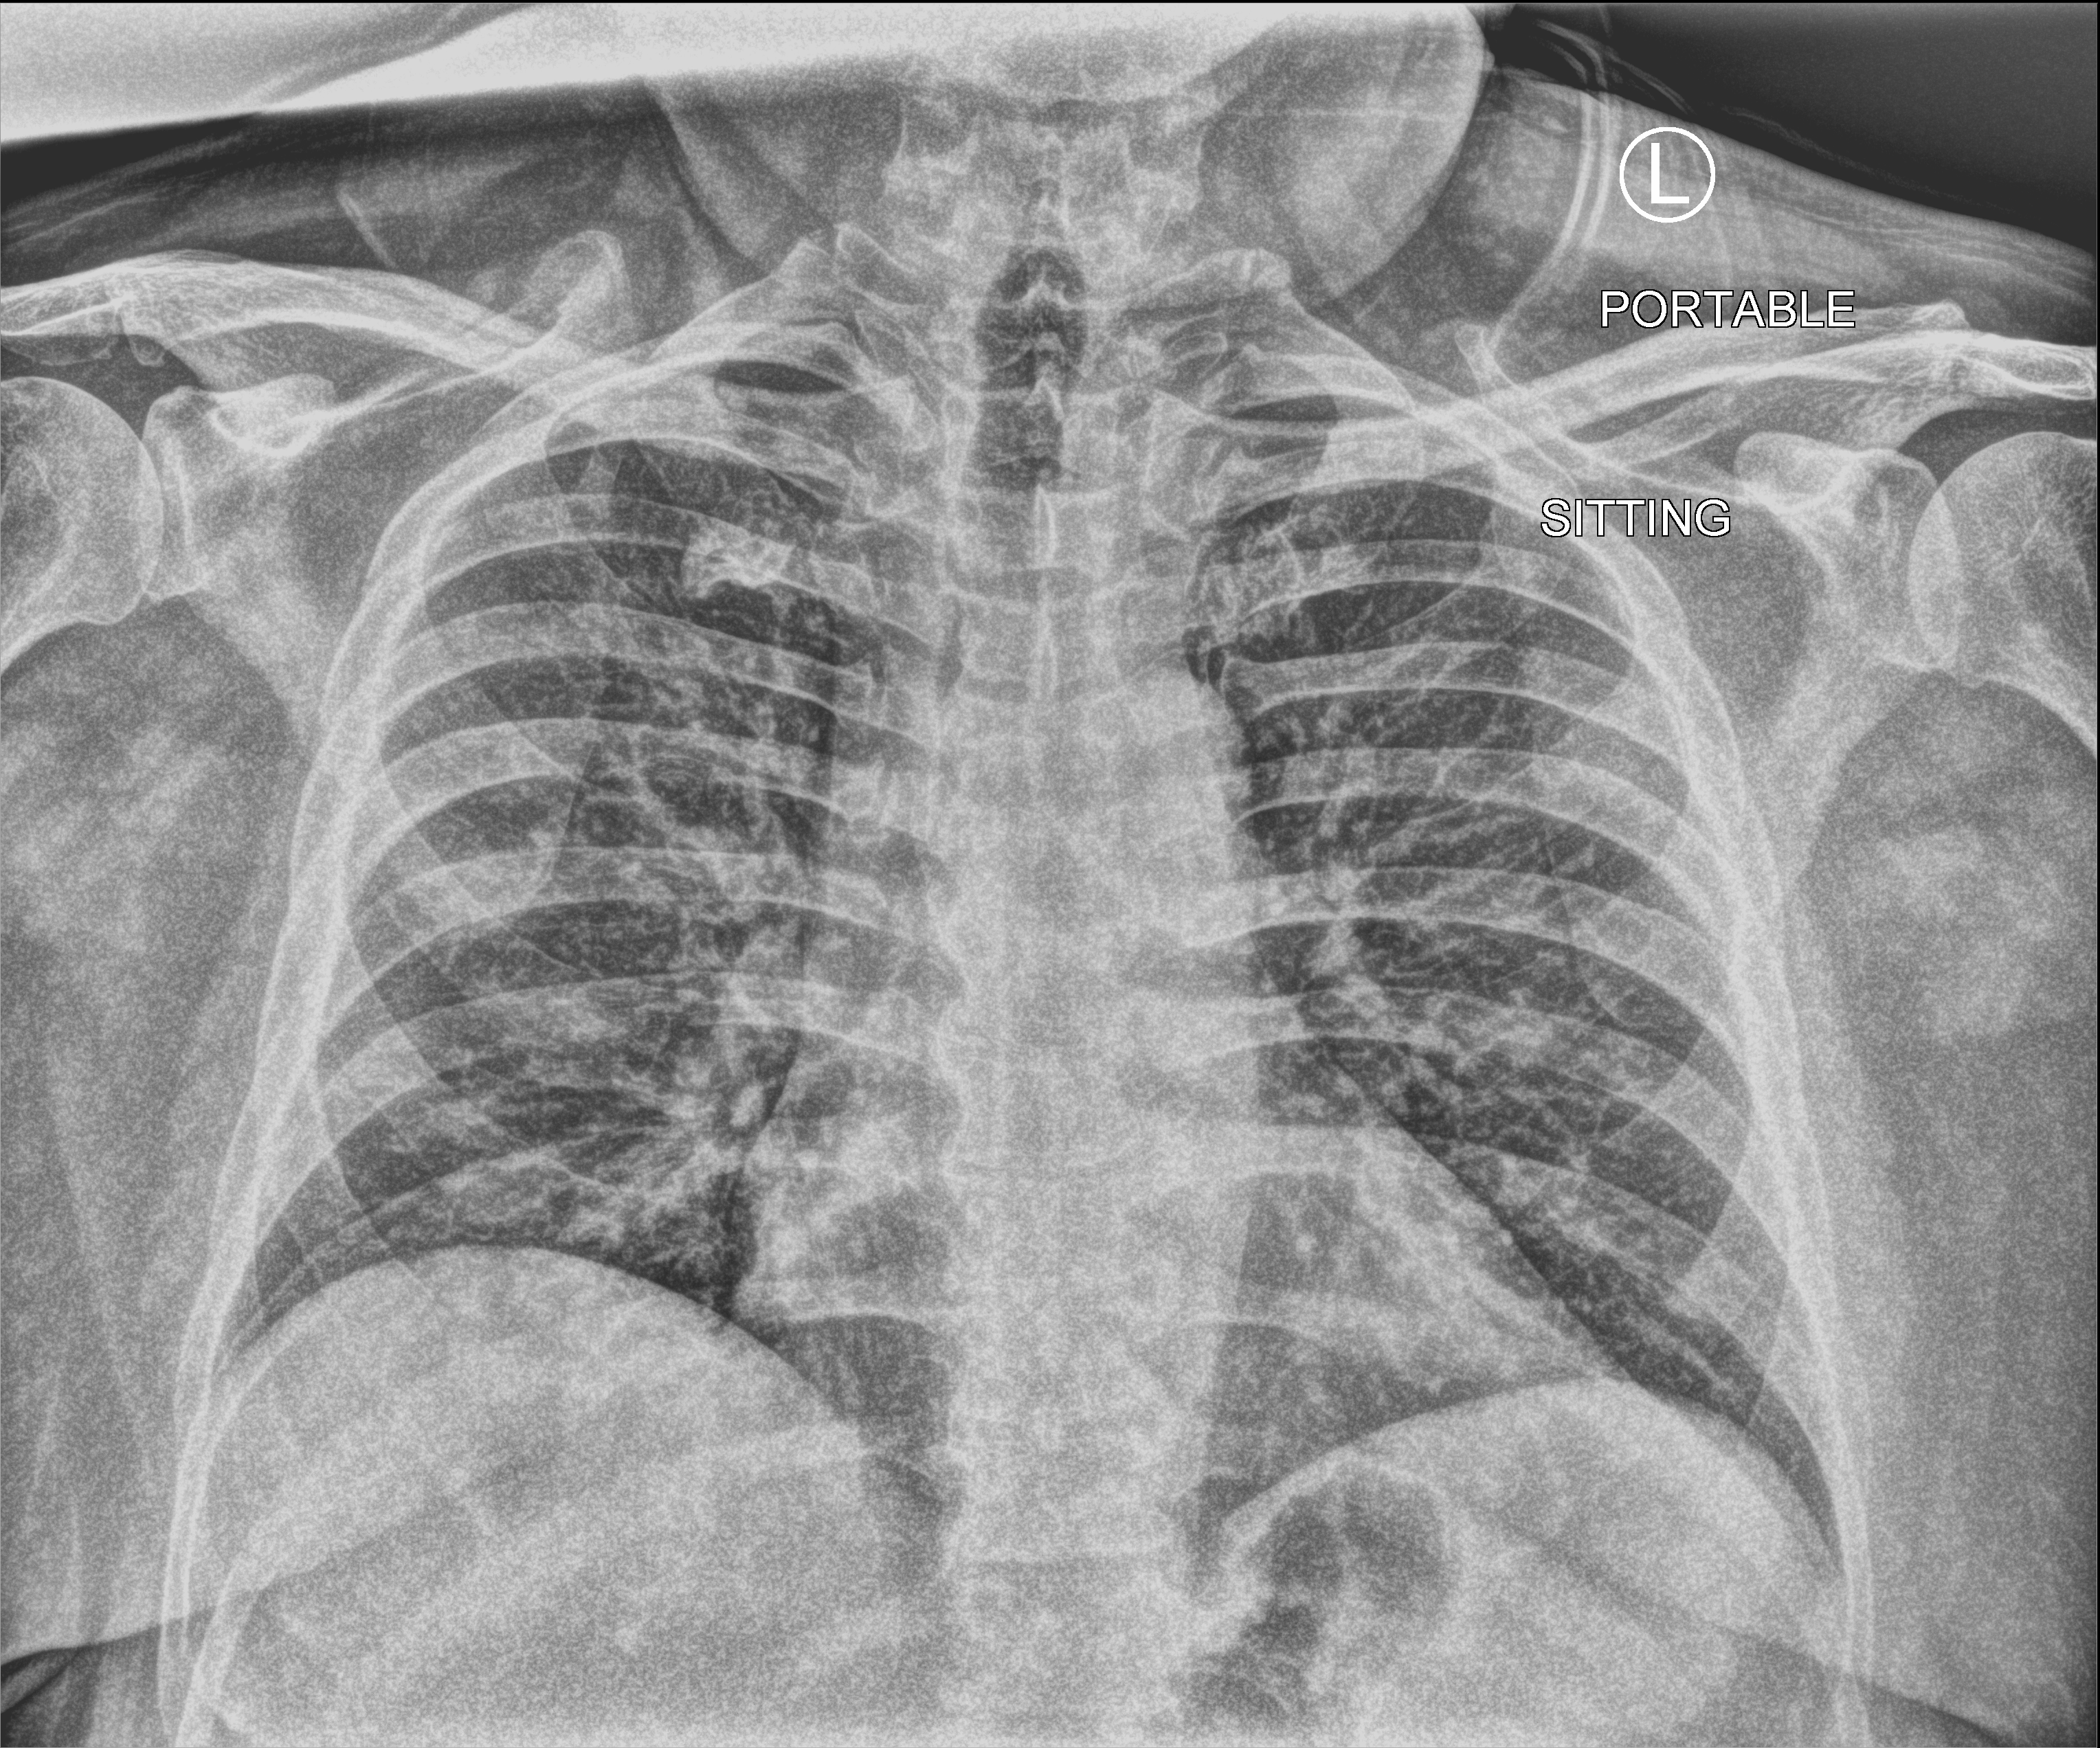
Chest X-ray (portable), anteroposterior (AP) projection. Male patient hospitalised with COVID-19, age 60–74 years.
Hospital-stay facts (about this admission, not read from this image; timing relative to this image not recorded):
- chronic kidney disease (admission record): no
- admitted to intensive care during this hospital stay: no